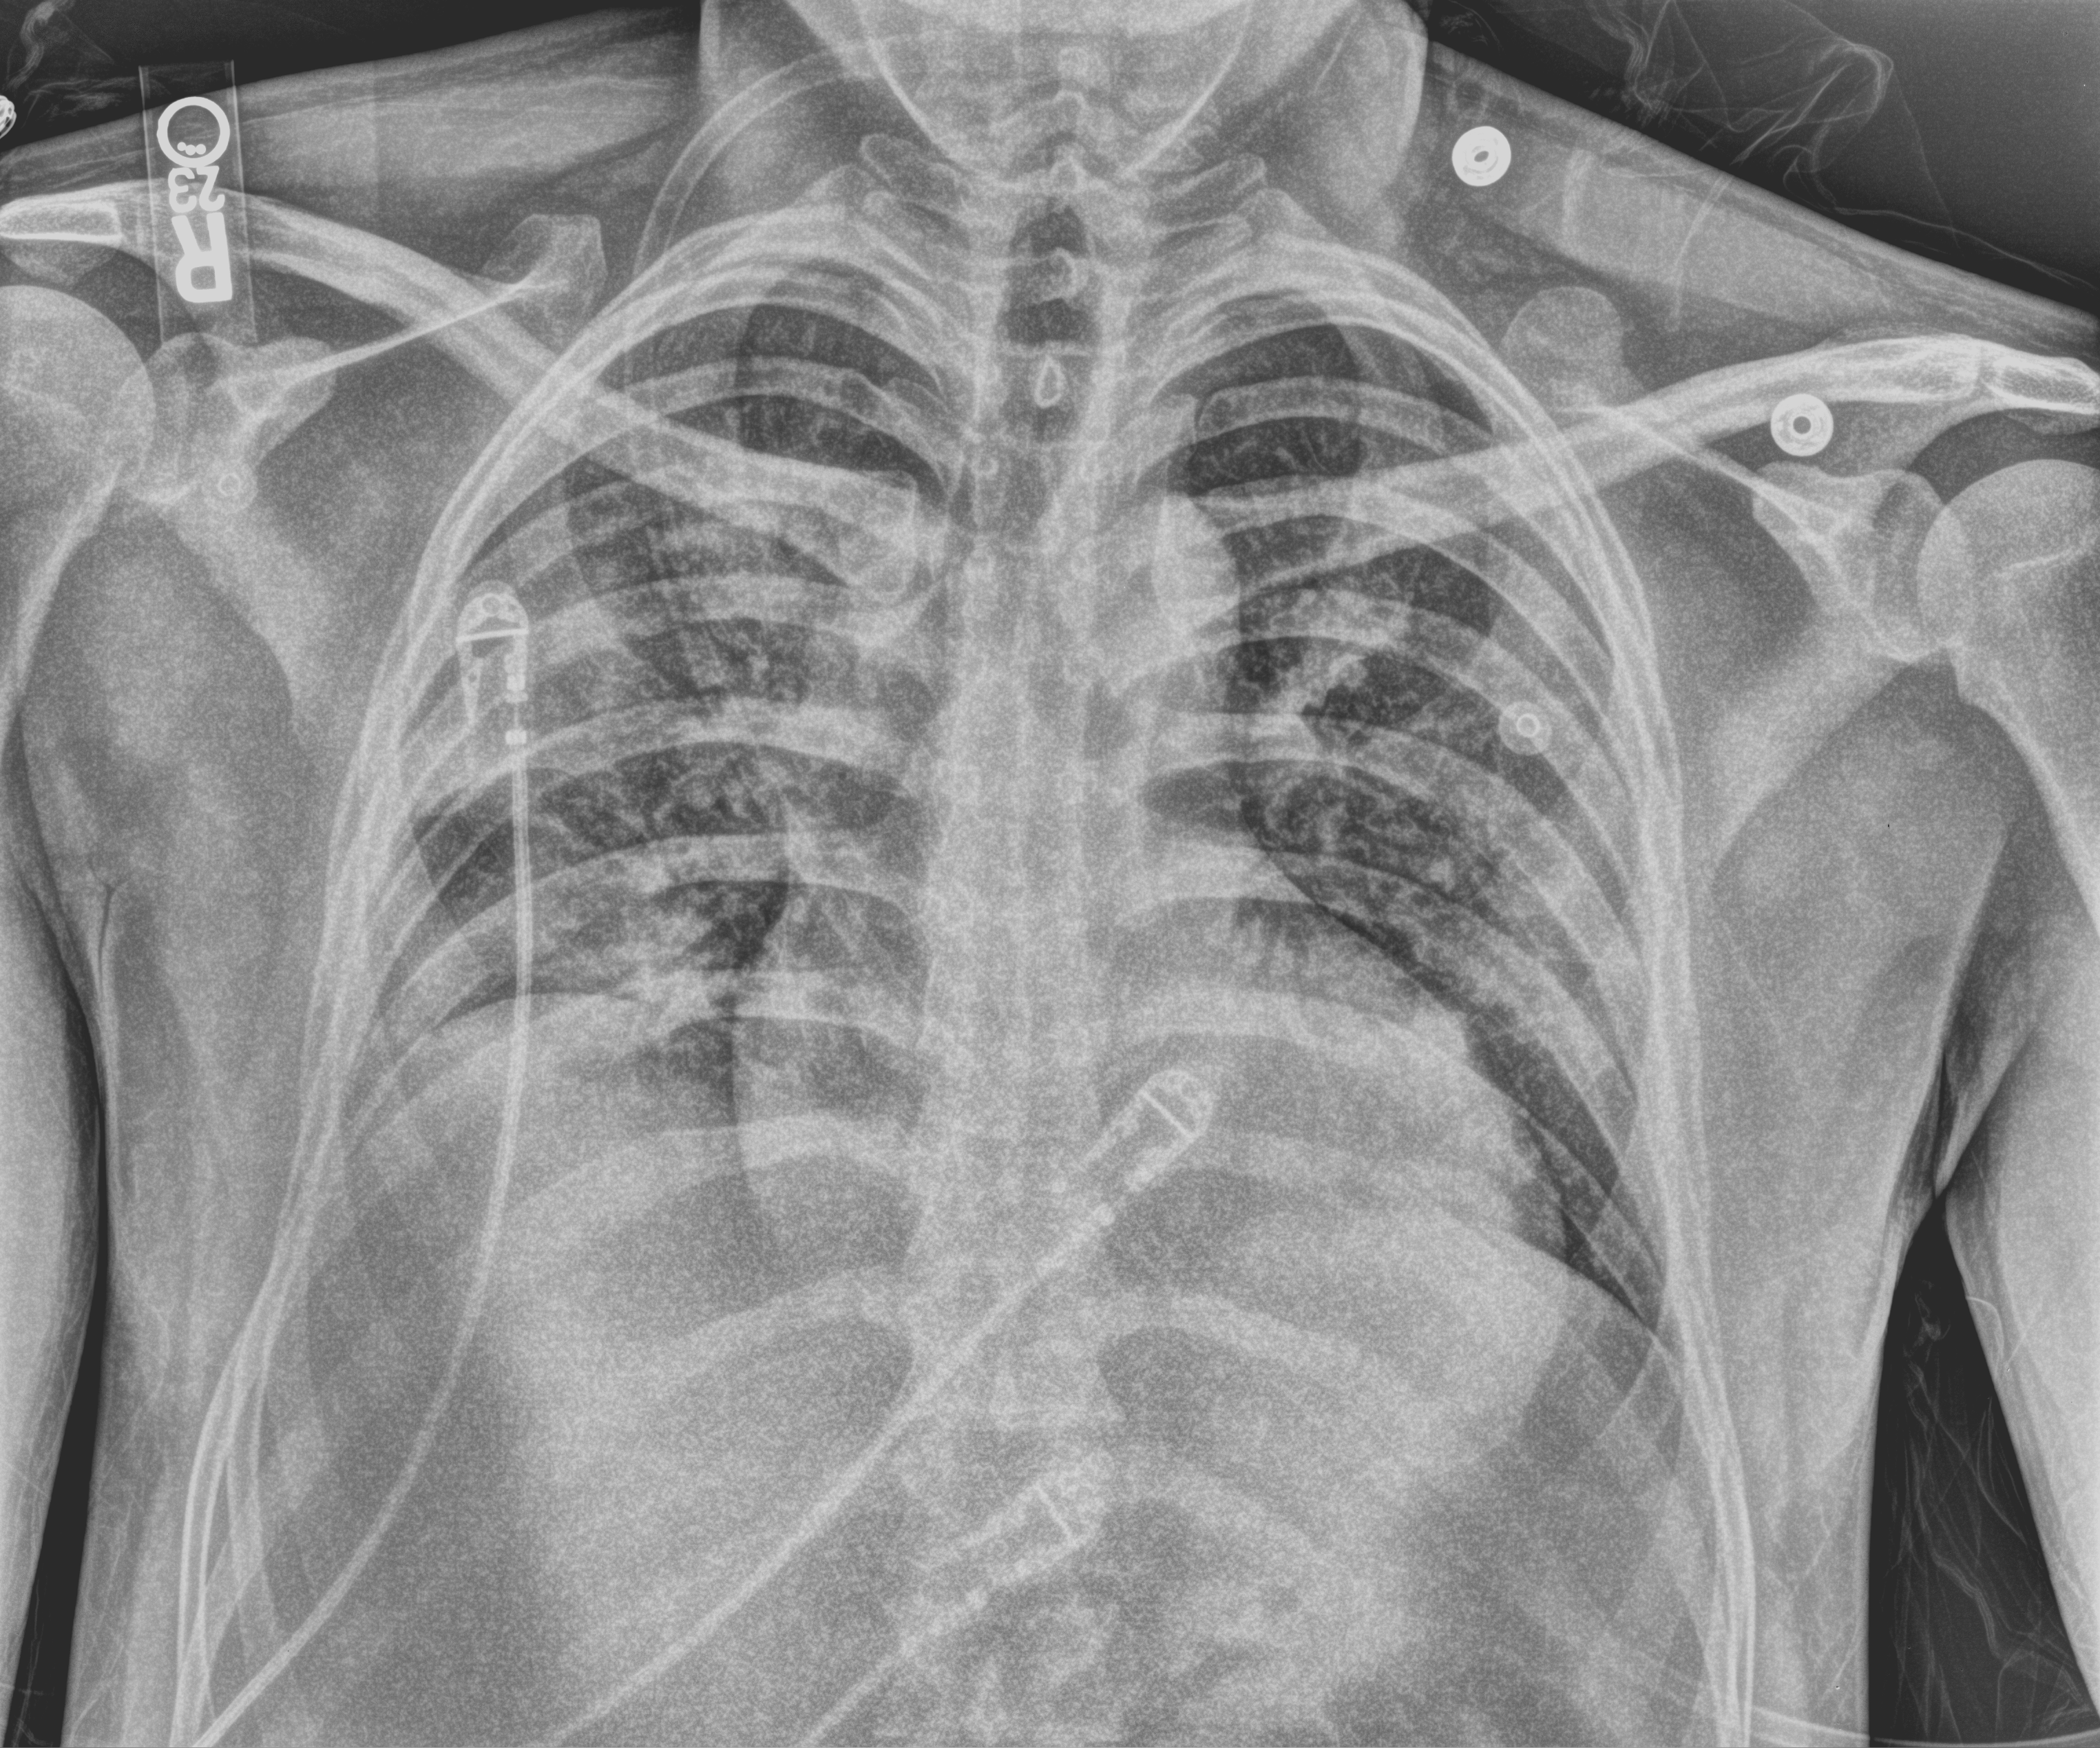
Chest X-ray (portable), anteroposterior (AP) projection. Patient hospitalised with COVID-19; male, aged 18–59 years.
From the hospital-stay record, not from the radiograph (when in the stay this image was taken is not recorded): smoking status (admission record): former.